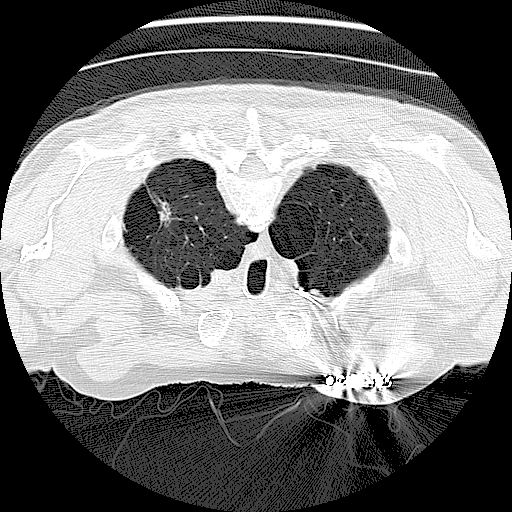
Low-dose screening chest CT, one axial slice; 120 kVp; lung window (W 1500 / L -600 HU); 2.5 mm slice thickness; 512 × 512 image matrix, field of view 330 × 330 mm.
Outlined on this slice (outlined manually by an expert reader):
- lesion 1 (tumor): bounding box (x1, y1, x2, y2) in pixels: (154, 198, 175, 227)